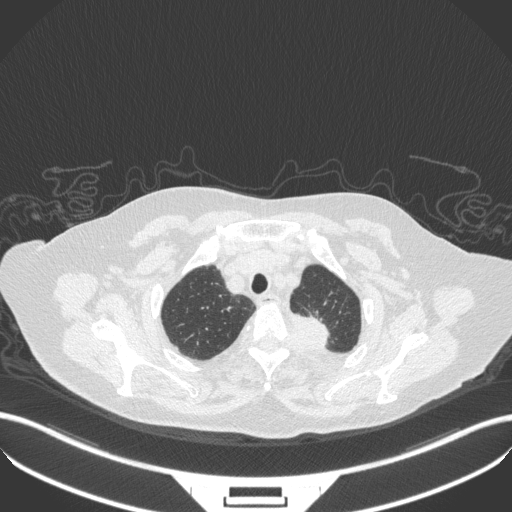
Chest CT, one axial slice; slice 299 of 353 in the series (ordered by position); reconstruction kernel B31f; 100 kVp; lung window (W 1500 / L -600 HU); 1 mm slice thickness; 512 × 512 image matrix, field of view 400 × 400 mm. Female patient, age 81 years. From the clinical record (not read from this slice): clinical TNM (as recorded): T2a N0 M0.
Annotated regions visible in this slice (rectangle marked by the reading radiologist):
- lung tumour (recorded histology: adenocarcinoma): bounding box [x1, y1, x2, y2] px = [283, 306, 334, 350]